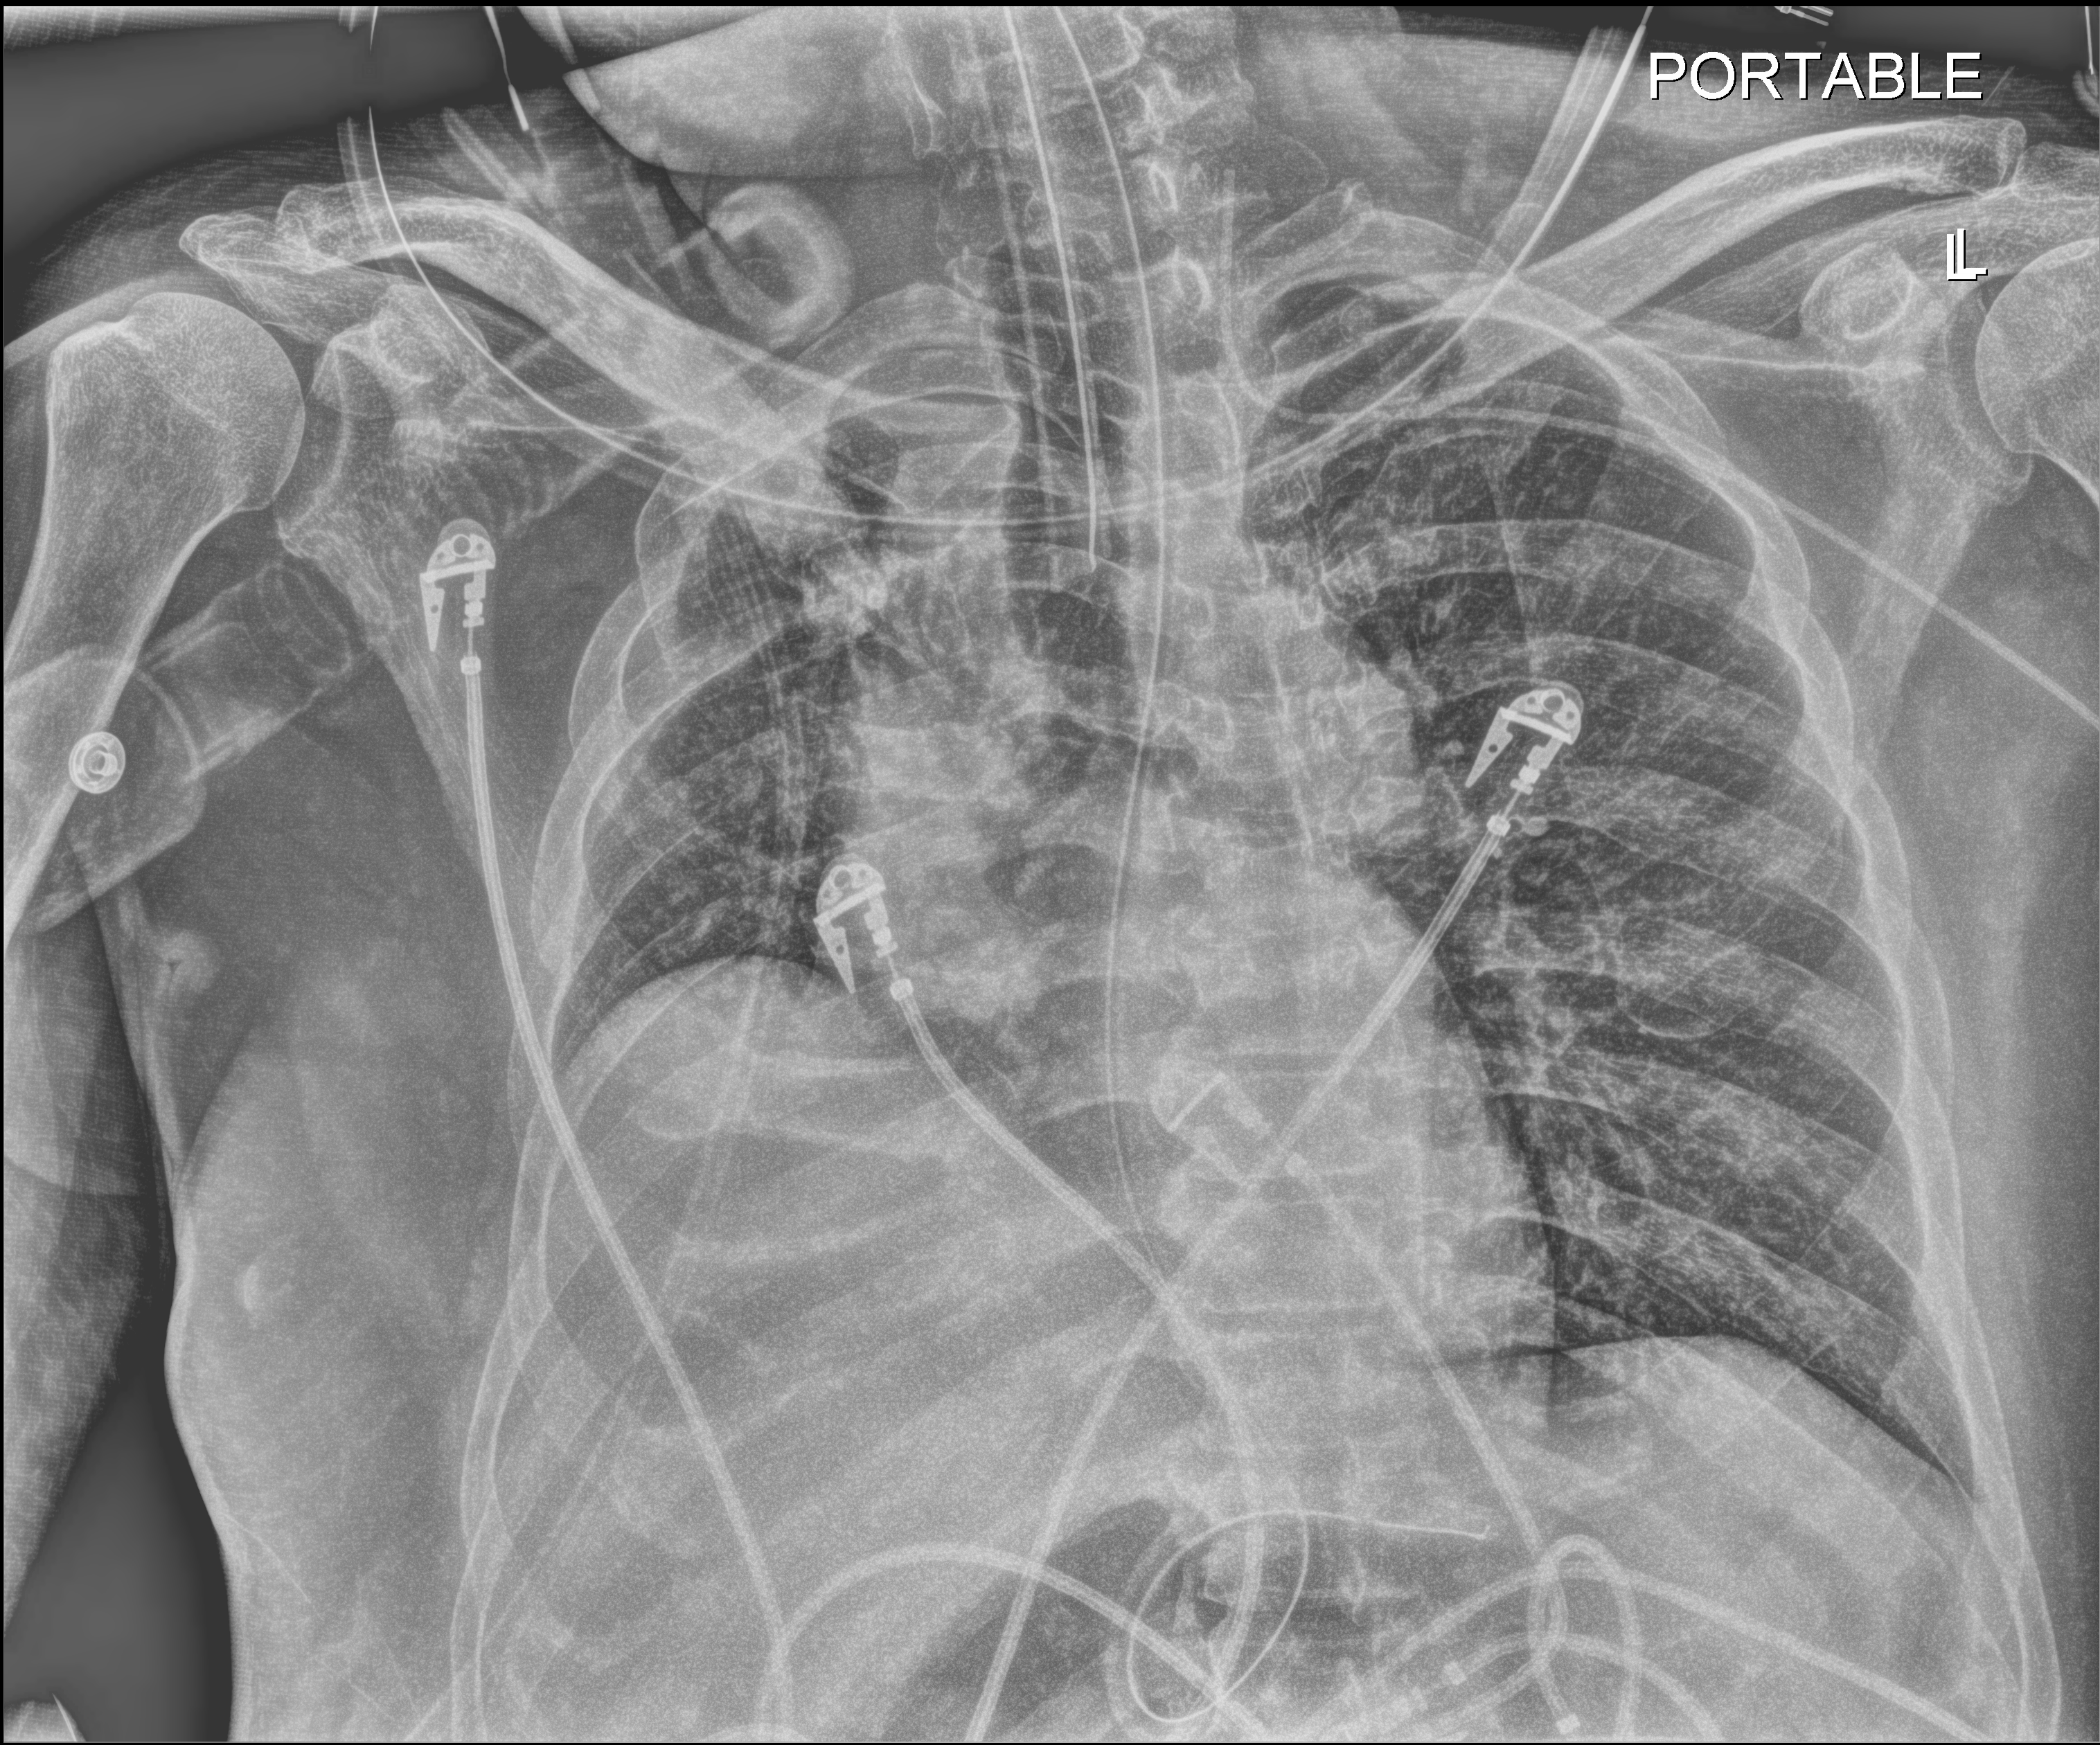
Bedside chest radiograph (digital radiography); anteroposterior (AP) projection. Patient hospitalised with COVID-19, aged 18–59 years.
Hospital-stay facts (about this admission, not read from this image; timing relative to this image not recorded): COPD (admission record): no; mechanically ventilated during this hospital stay: yes; admitted to intensive care during this hospital stay: yes.